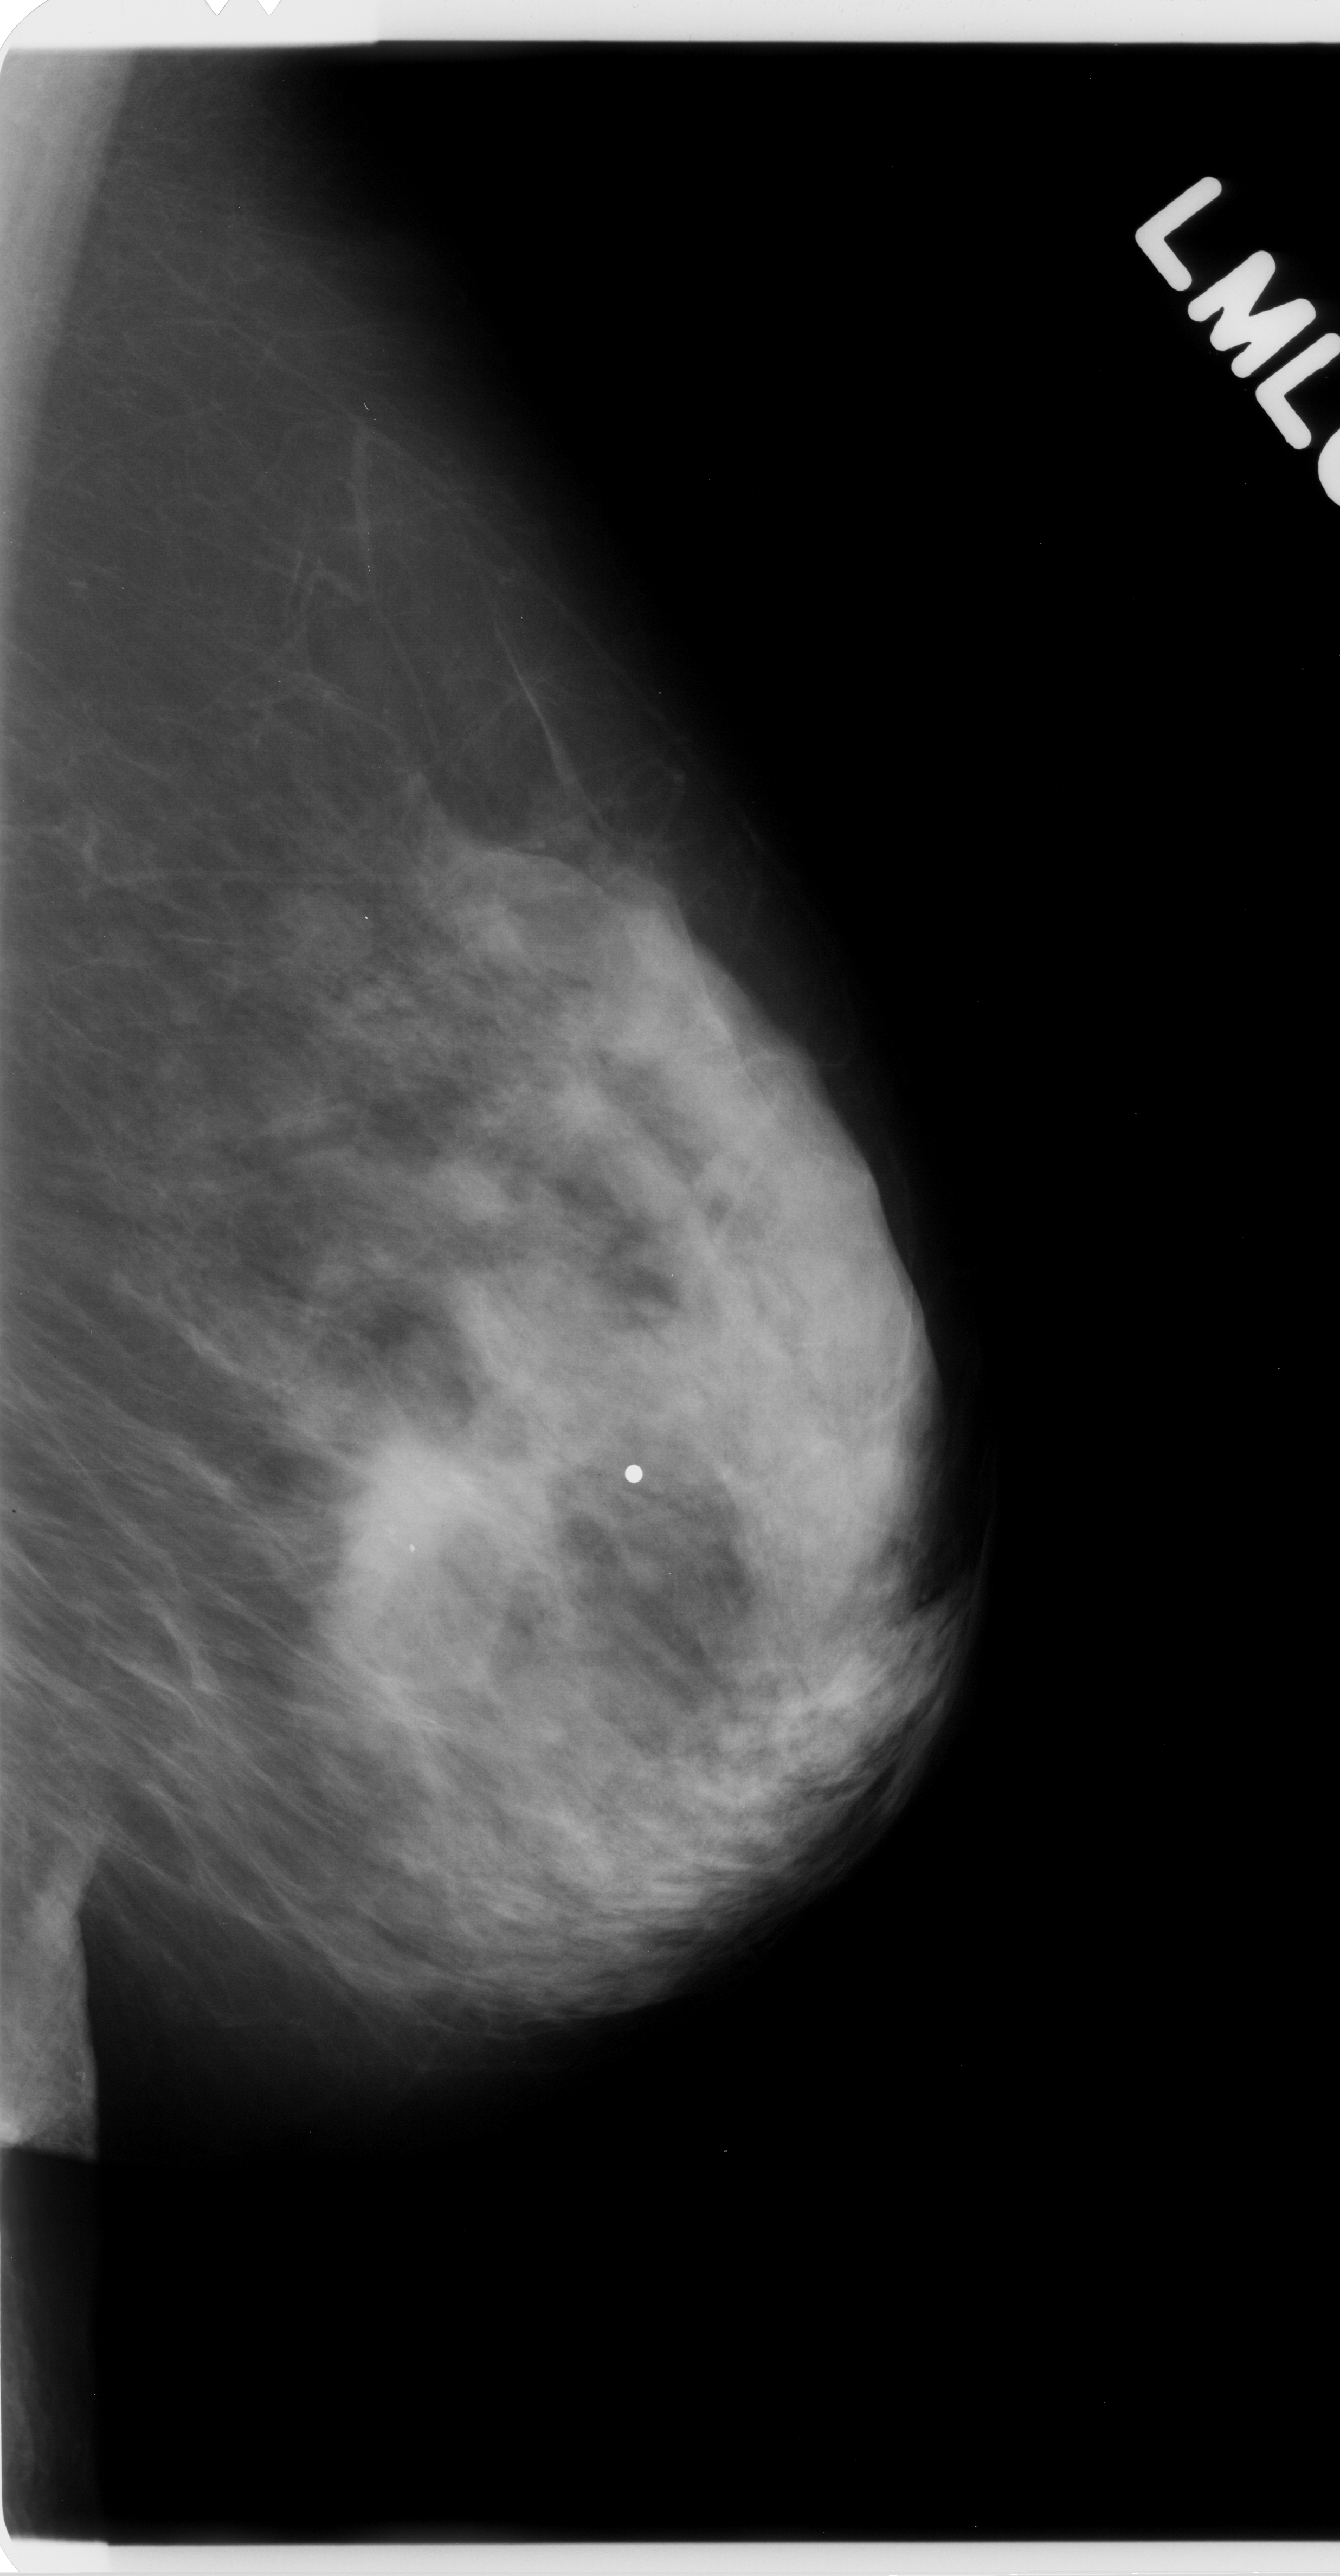
Digitized screen-film mammogram, left breast, MLO view, BI-RADS breast density category 3 (scale 1–4).
Mass, shape round, margins spiculated; BI-RADS assessment category 5; subtlety rating 5 on a 1 (subtle) to 5 (obvious) scale; pathology (as recorded): malignant.